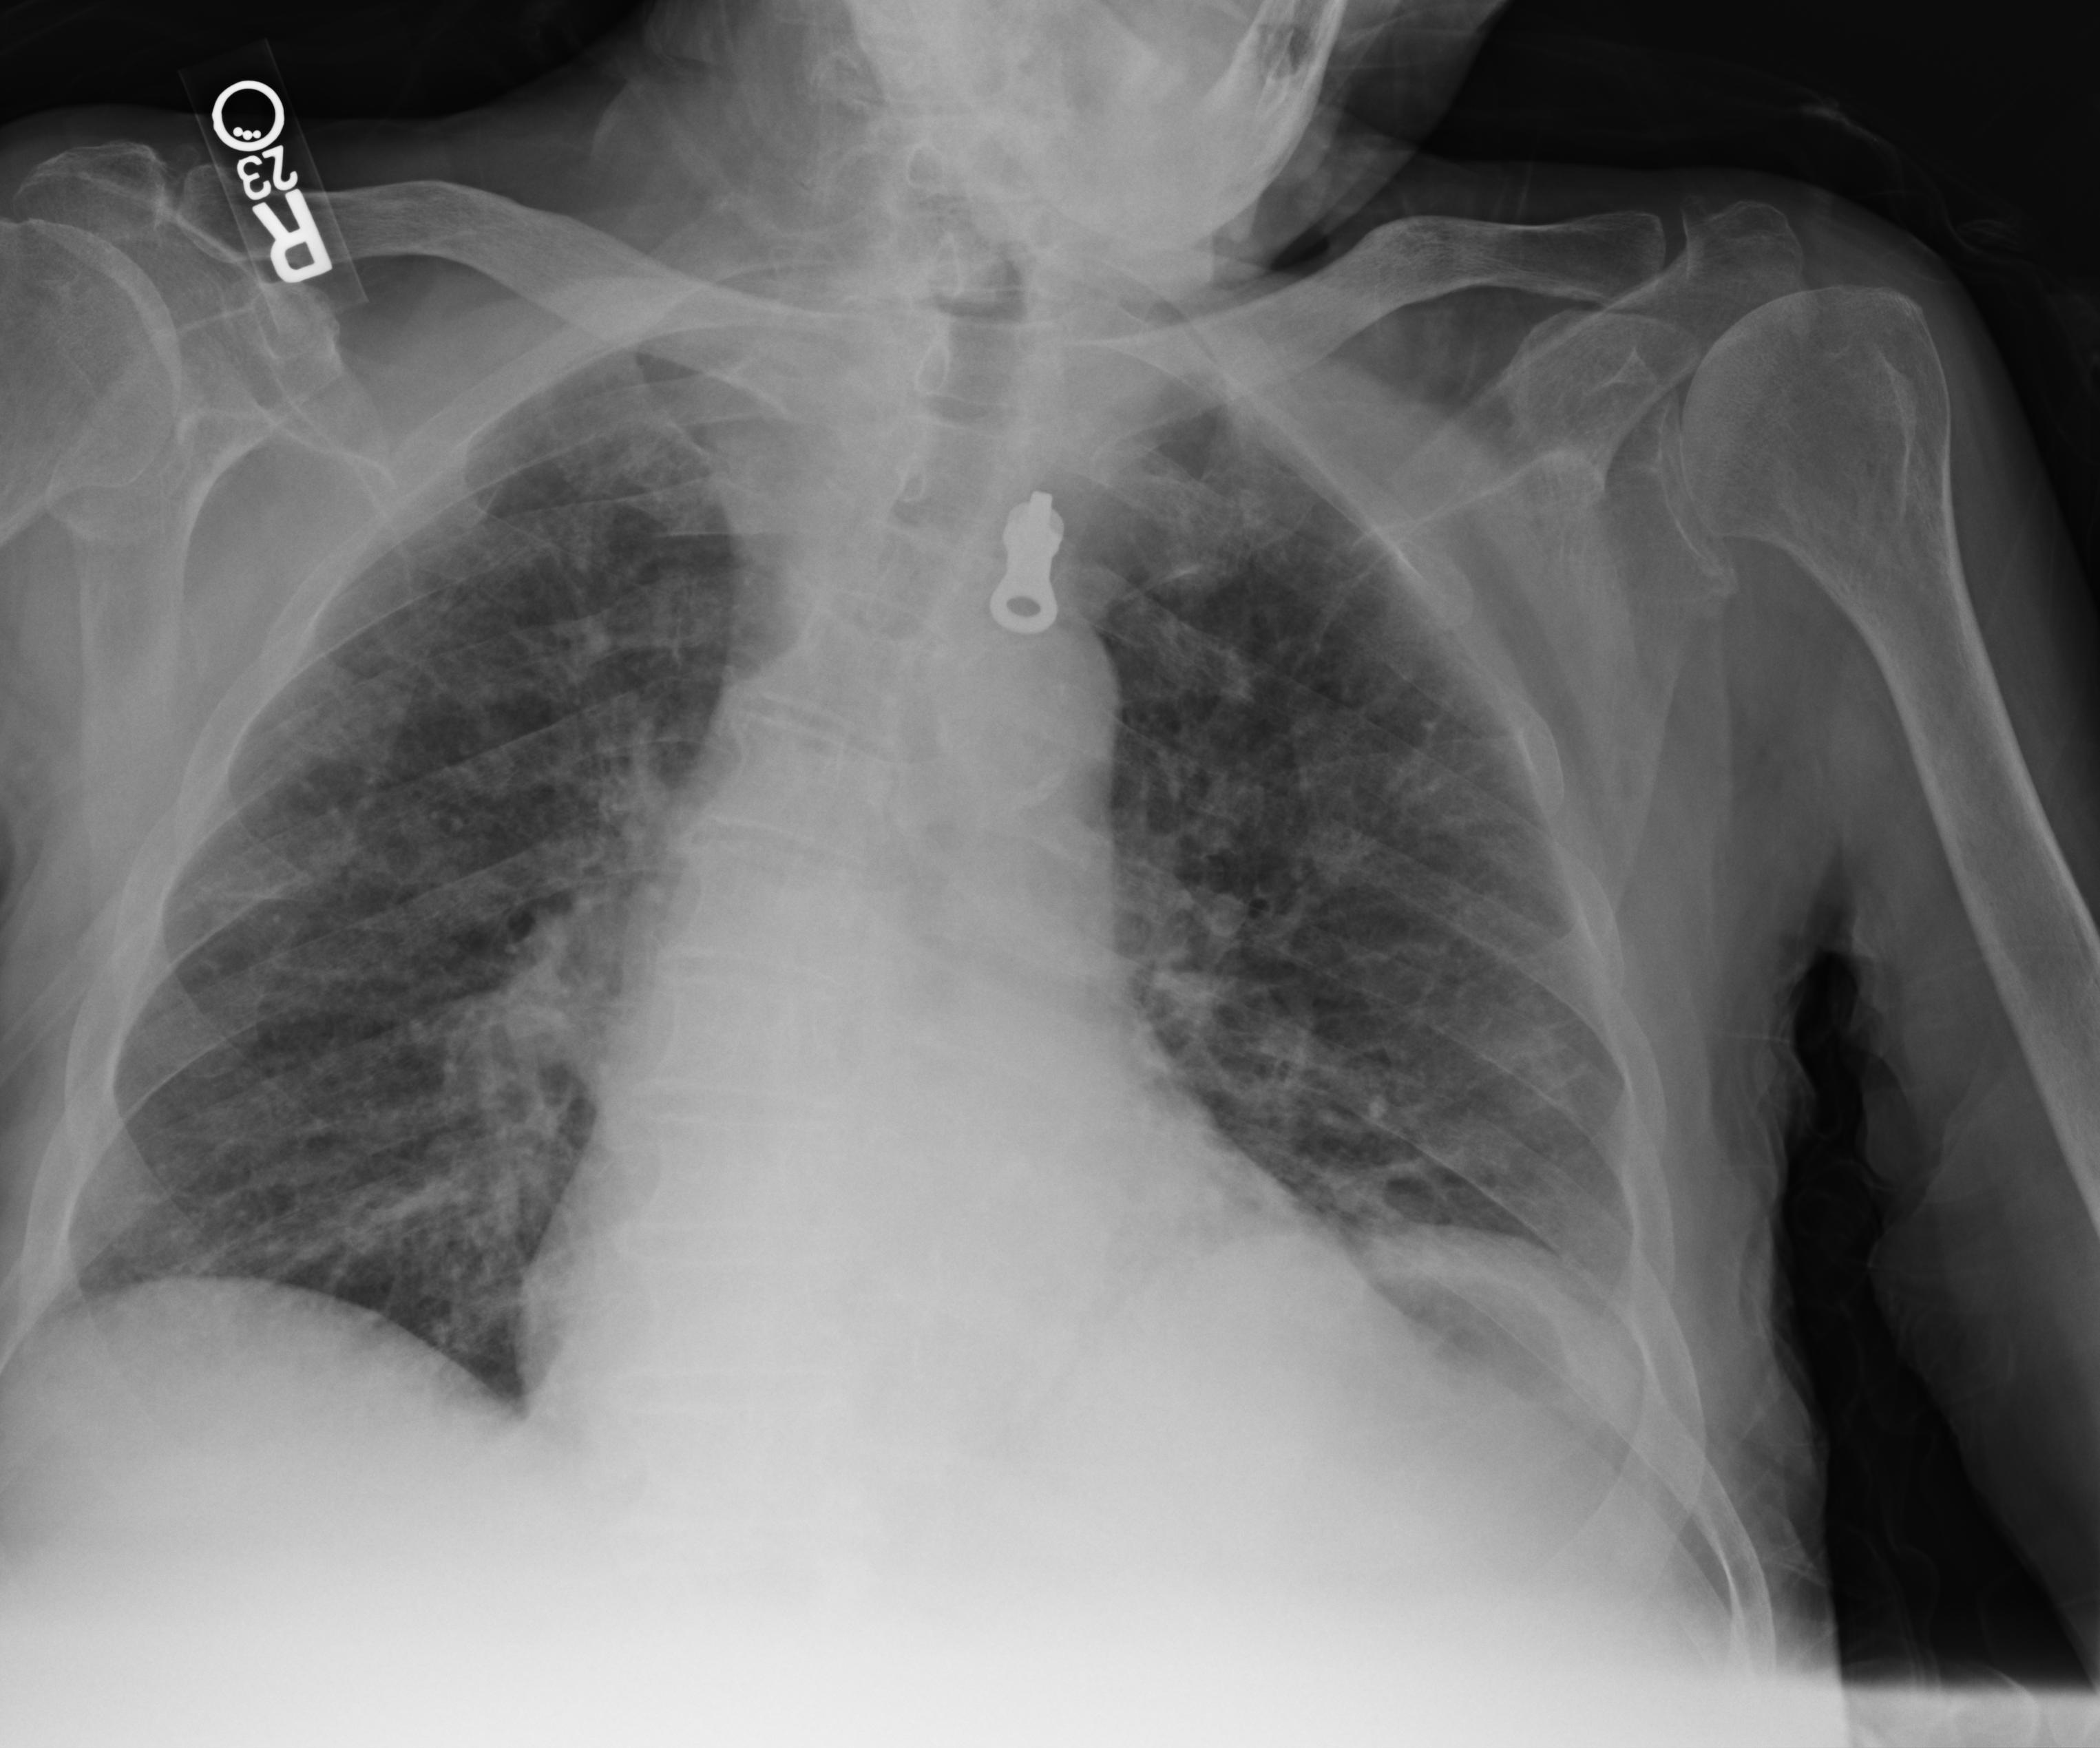
Bedside chest radiograph (computed radiography), anteroposterior (AP) projection. Male patient hospitalised with COVID-19, age 75–90 years.
From the hospital-stay record, not from the radiograph (when in the stay this image was taken is not recorded):
- admitted to intensive care during this hospital stay: no
- mechanically ventilated during this hospital stay: no